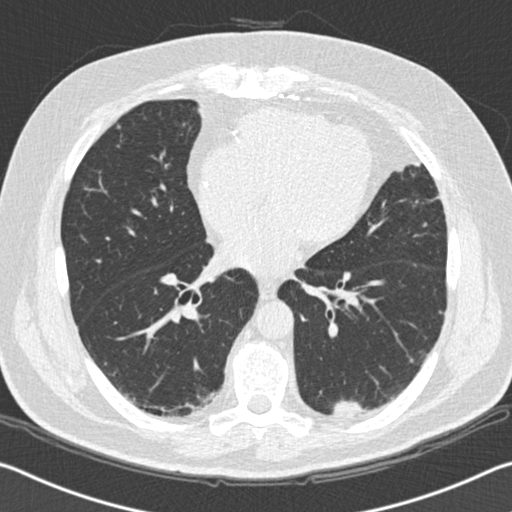
Low-dose screening chest CT, axial slice; second annual screen; lung window (W 1500 / L -600 HU); 120 kVp; 512 × 512 image matrix, field of view 340 × 340 mm. Male, age 65 years at enrolment. Former smoker at enrolment.
Expert-annotated lung lesion, box from (x=325, y=388) to (x=388, y=435) px. Reader record for this screening exam (exam-level; its link to the box is not recorded): non-calcified nodule or mass ≥4 mm, left lower lobe, 19 × 11 mm, spiculated (stellate) margins, soft tissue attenuation, pre-existing on the prior screen: yes; interval growth: yes. Later outcome: lung cancer diagnosed 179 days after this screen — squamous cell carcinoma, NOS, left lower lobe, moderately differentiated (G2), stage IA (AJCC 6th edition), 20 mm at pathology.